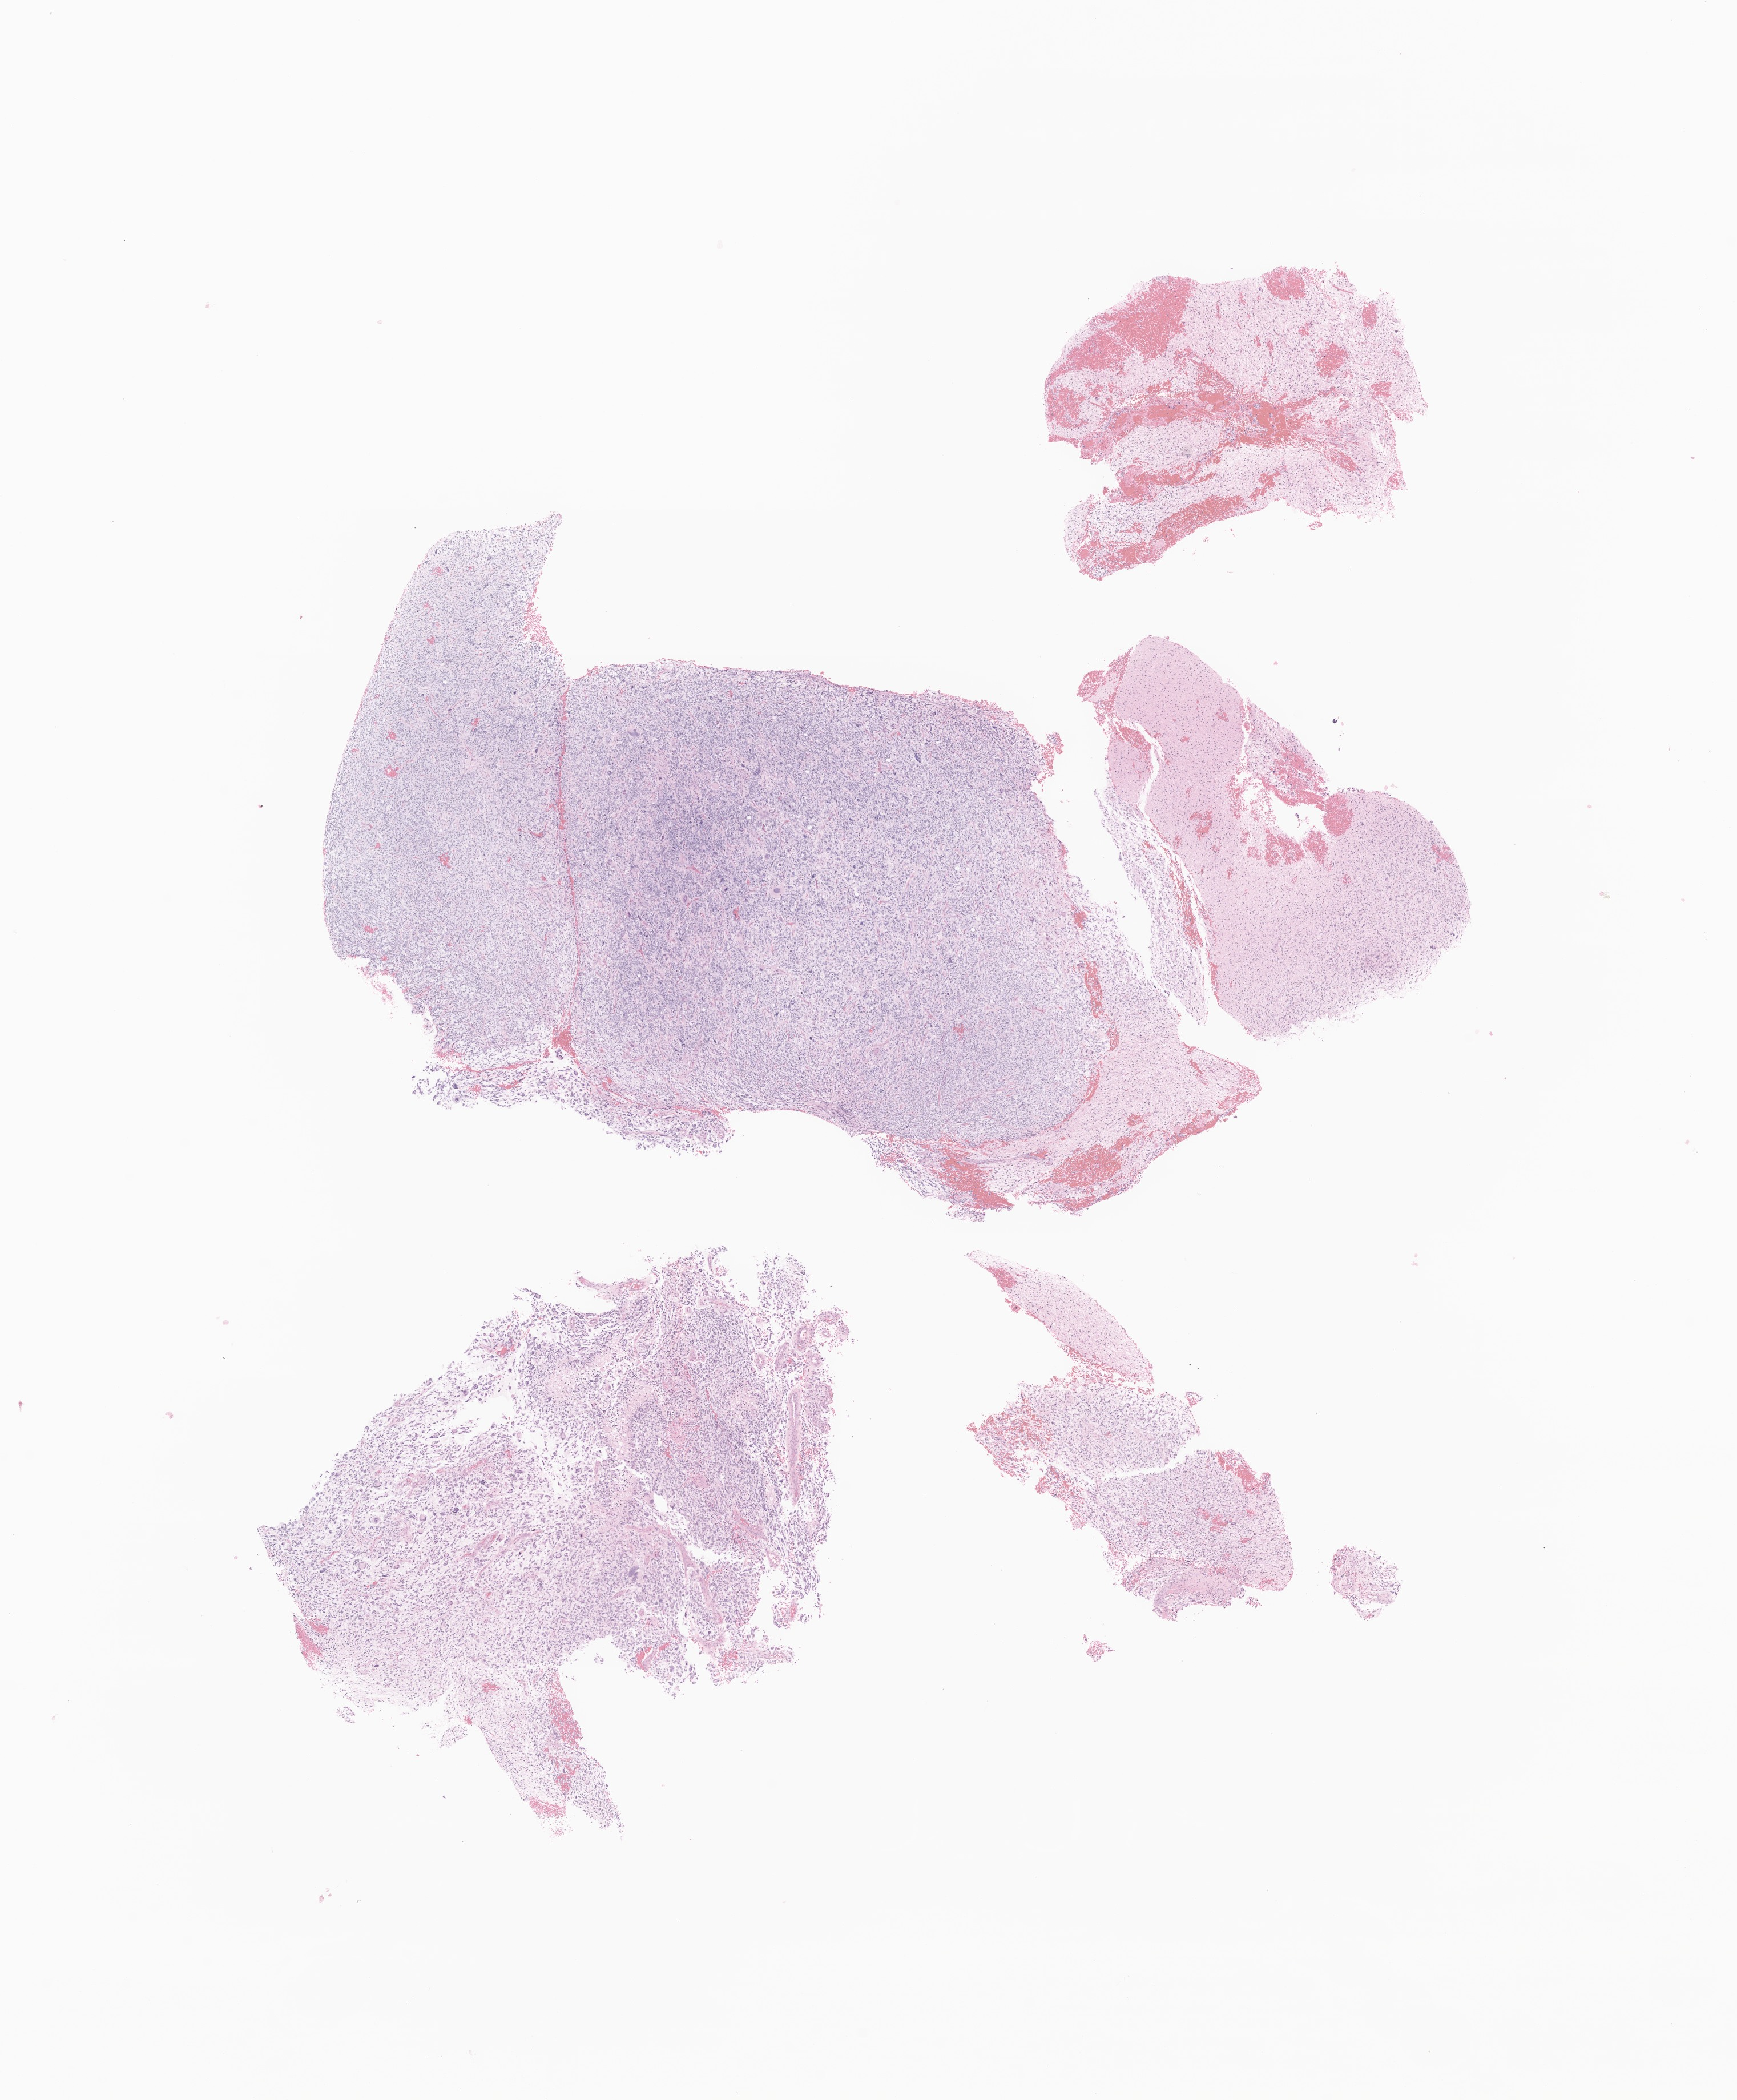
Hematoxylin and eosin (H&E) whole-slide image of tumor tissue from the frontal lobe — a low-resolution overview of the entire scanned area, about 12.8 x 15.5 mm. Formalin-fixed, paraffin-embedded (FFPE) tissue. Patient: male, age 206 months (17 years 2 months).
Diagnosis (ICD-O-3 morphology term): Glioma, malignant.